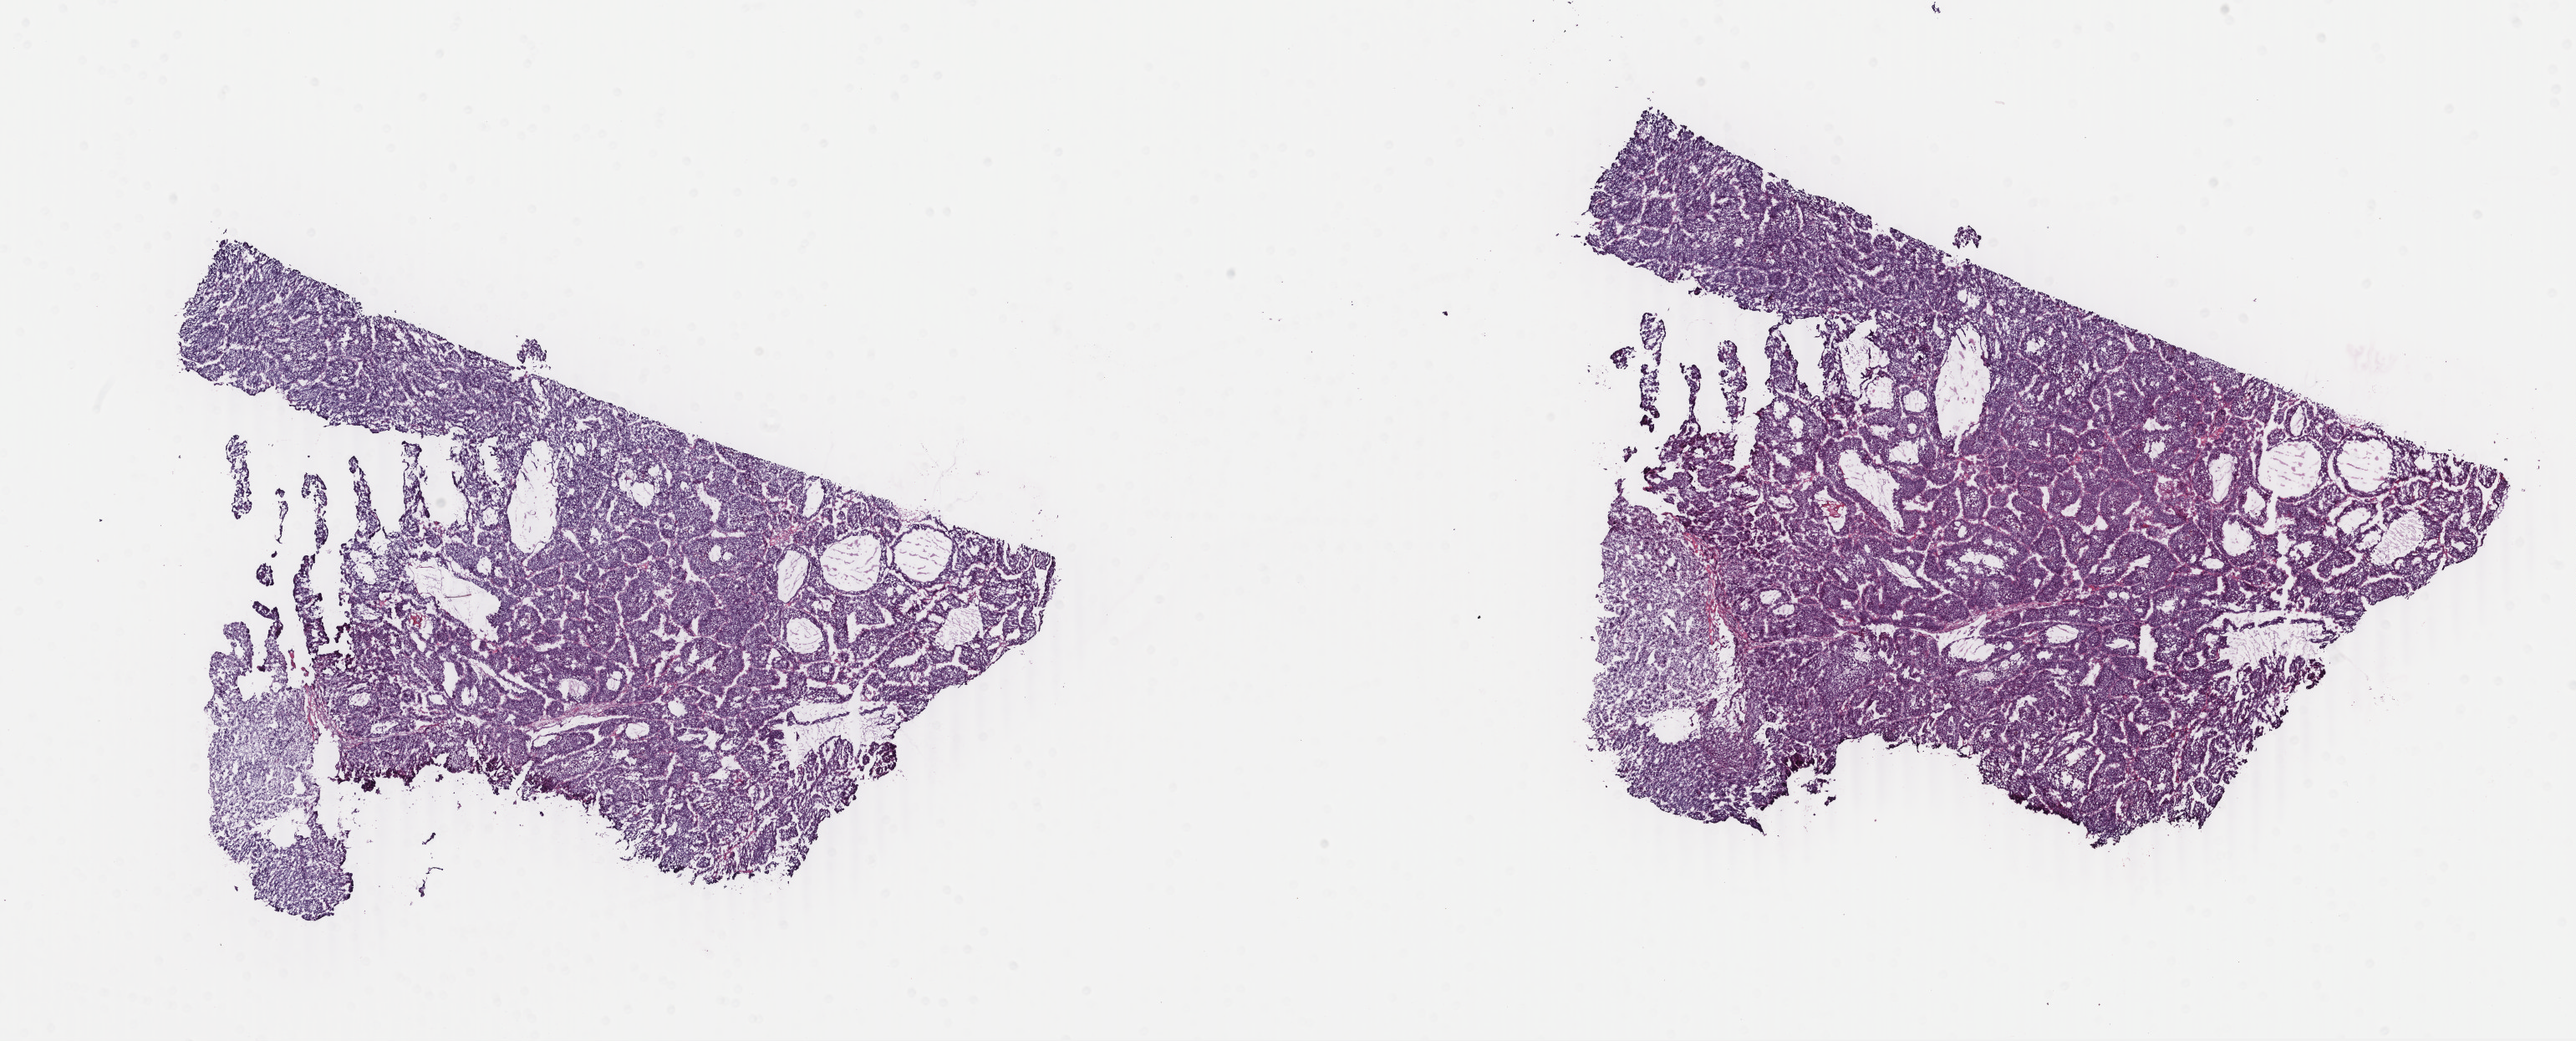
Digitized Hematoxylin and eosin (H&E) stained tissue section (whole slide), whole scanned area (about 24.5 x 9.9 mm) shown as a low-resolution overview; frozen section; liver, primary tumour sample. Patient: female, age at initial diagnosis 24 years. Composition of this section per pathologist review: tumour cells 100%, tumour nuclei 95%.
Diagnosis: Hepatocellular carcinoma, NOS.